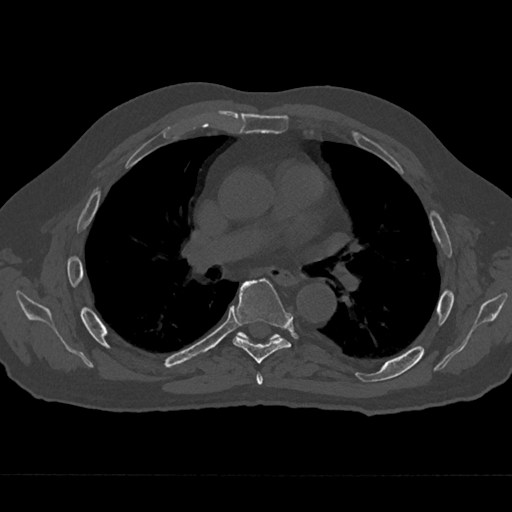
CT including the spine, one axial slice; position 413 of 797 along the scan axis; 120 kVp; bone window (W 1800 / L 400 HU); 0.5 mm slice thickness; 512 × 512 image matrix. Male patient, age 75 years. Case-level facts recorded for this patient, not image findings: primary cancer: renal.
Annotated regions visible in this slice (semi-automatically segmented with operator editing):
- T5 vertebra: bounding box [x1, y1, x2, y2] px = [256, 373, 263, 385]
- T6 vertebra: [232, 278, 291, 364]
- T7 vertebra: [239, 332, 278, 340]